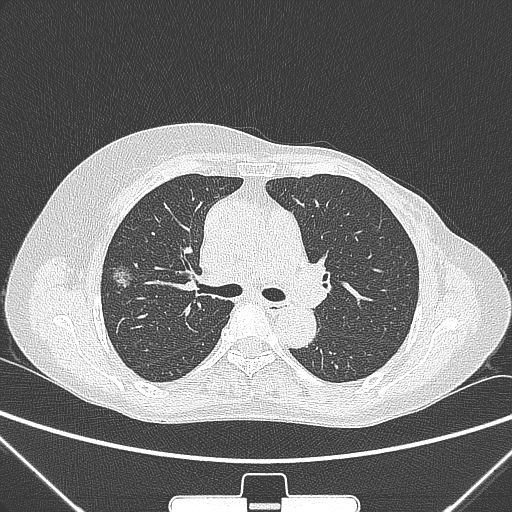
Chest CT, one axial slice. Position 159 of 265 along the scan axis. Lung window (W 1500 / L -600 HU). 1 mm slice thickness. 512 × 512 image matrix, field of view 350 × 350 mm. Patient: female, 64 years. From the clinical record (not read from this slice): clinical TNM (as recorded): T1c N0 M0; histopathological grade: G1-2.
Outlined on this slice (rectangle marked by the reading radiologist):
- lung tumour (recorded histology: adenocarcinoma): bounding box <106,259,136,295> (left, top, right, bottom; pixels)